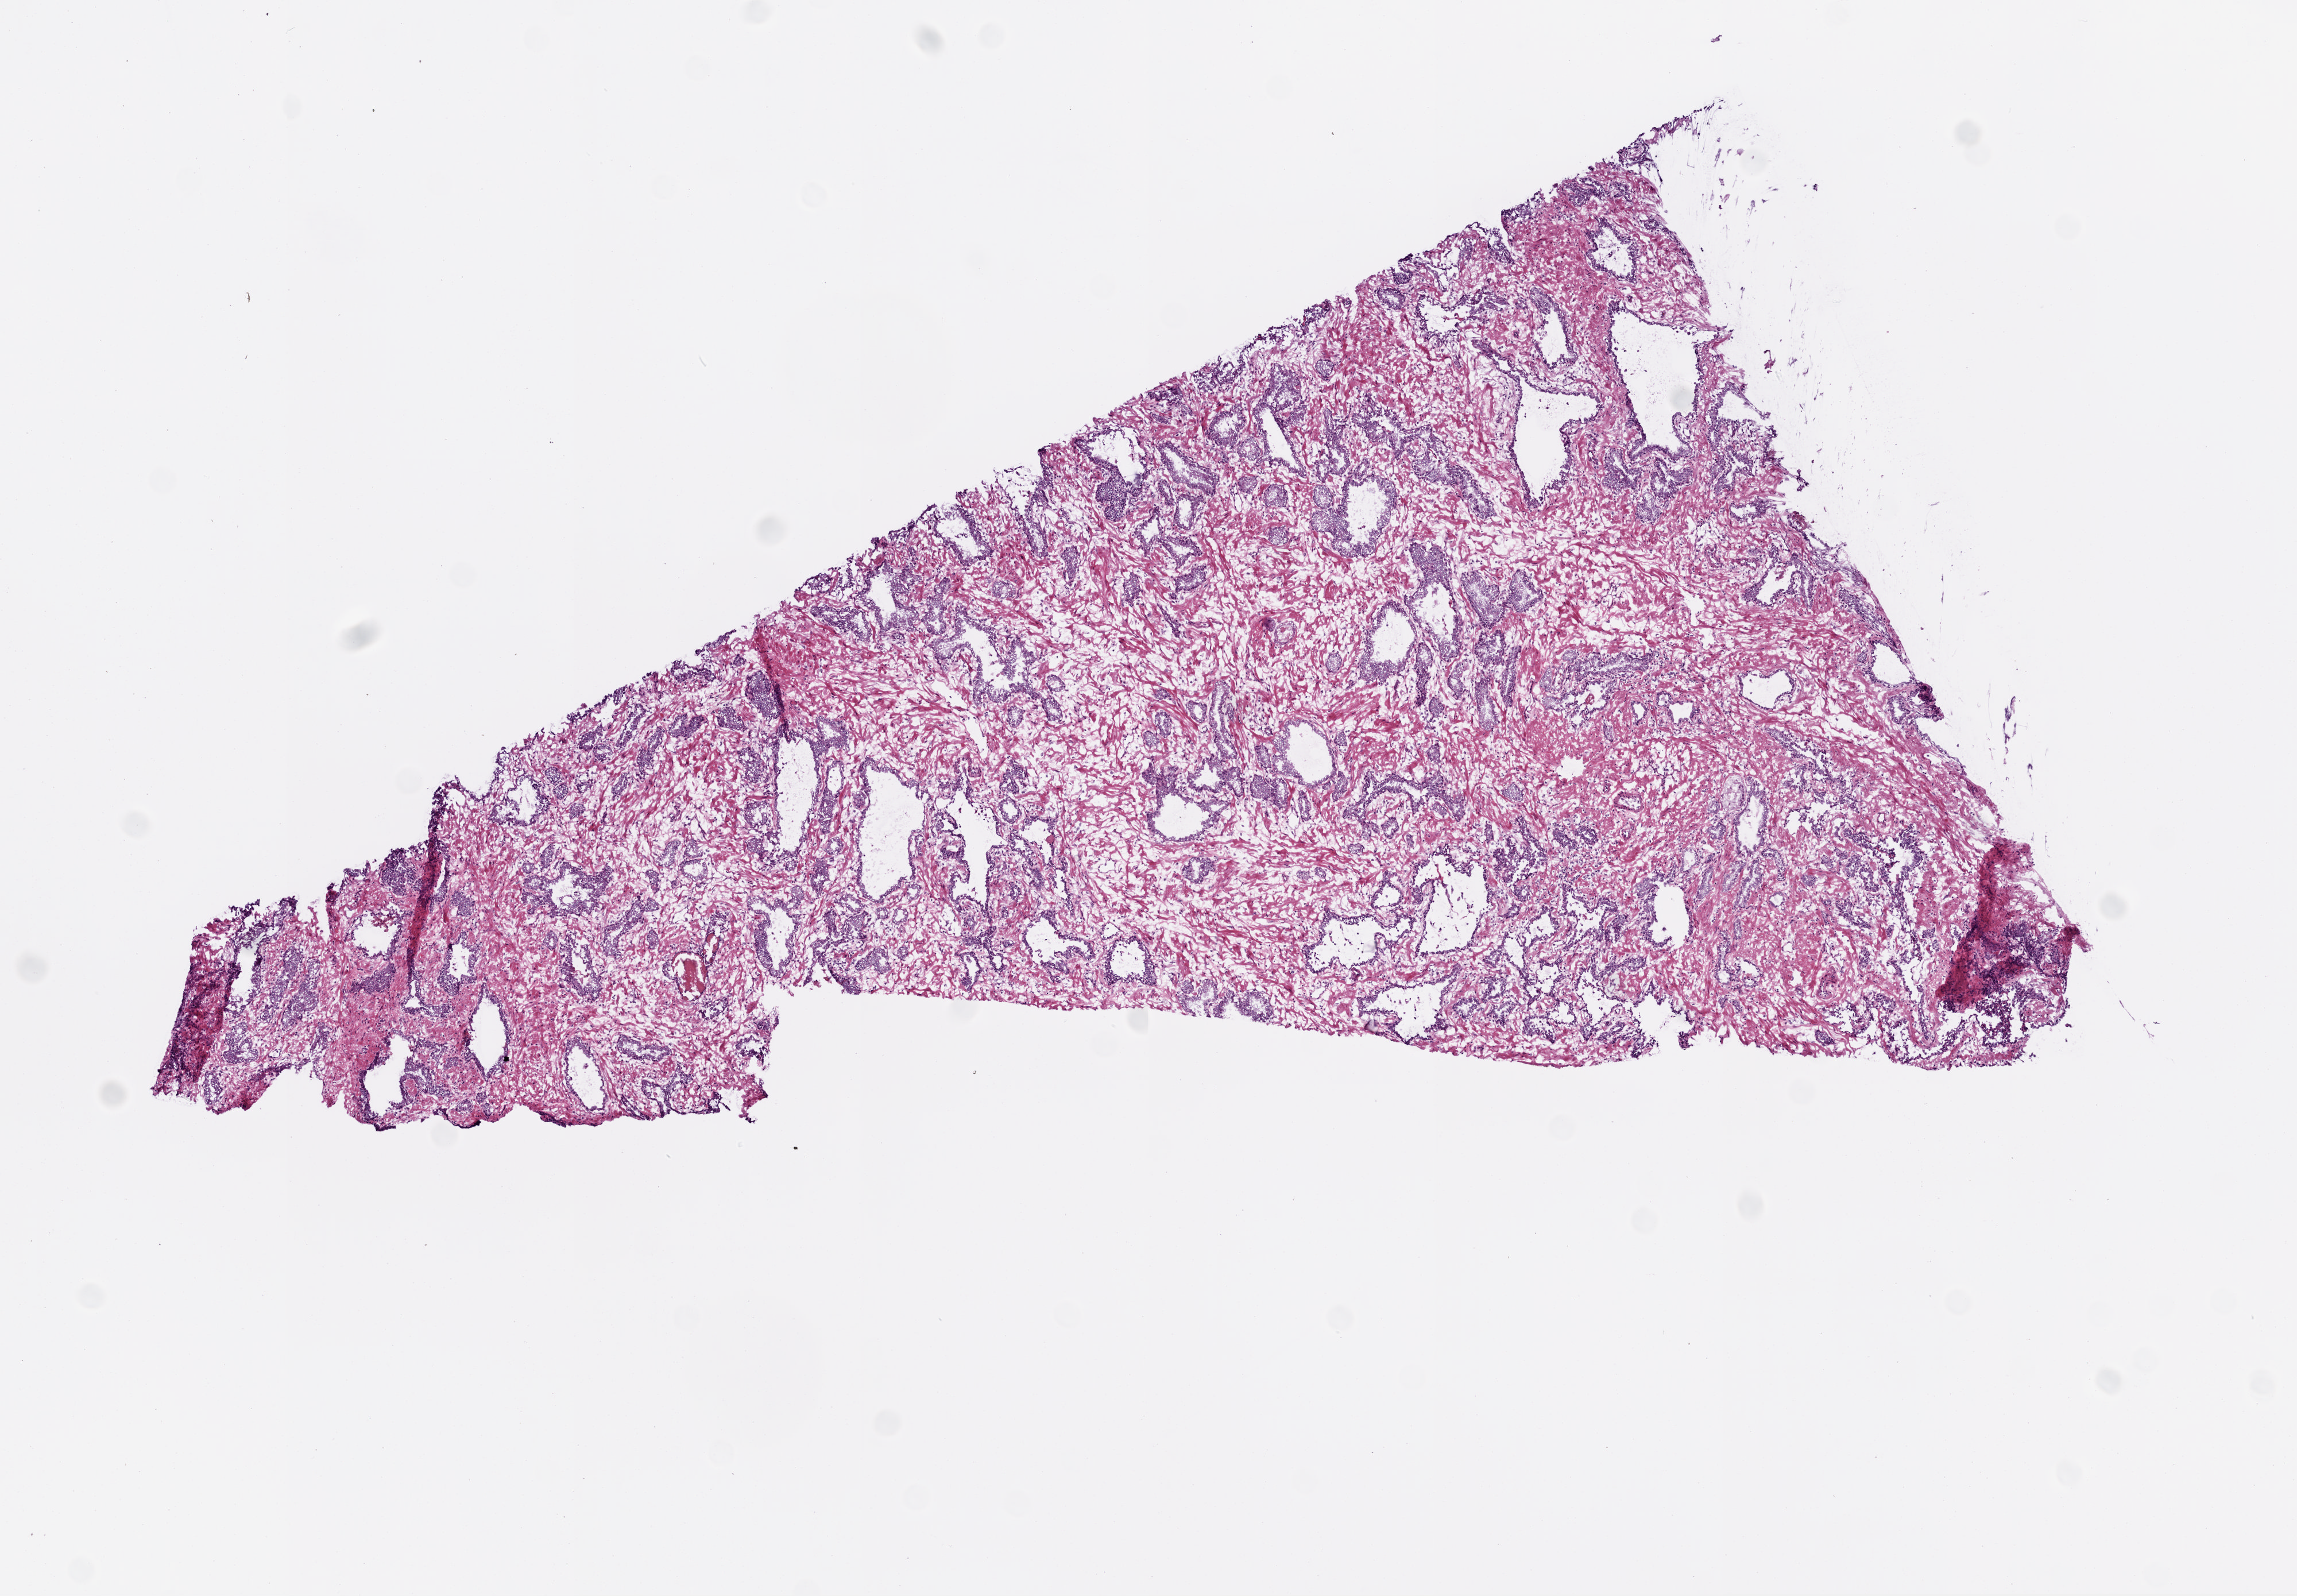
H&E whole-slide image, low-resolution overview of the scanned area, about 8.0 x 5.6 mm; frozen section; solid tissue normal (non-tumour tissue) sample from the prostate. Patient: male, age at initial diagnosis 63 years.
This section: solid tissue normal (non-tumour) sample from the same patient. Patient diagnosis: Acinar cell carcinoma (prostate gland).